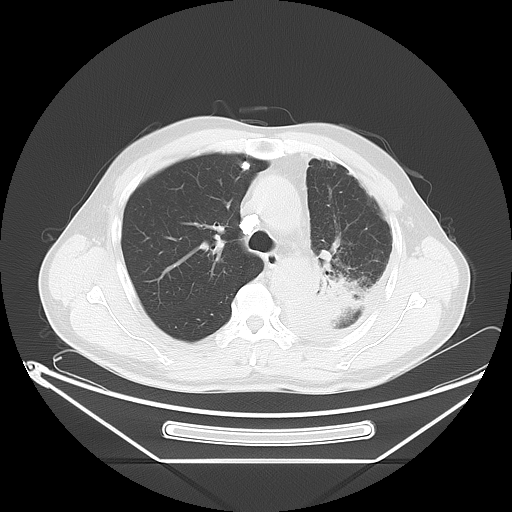
Chest CT, one axial slice. Slice 43 of 63 in the series (ordered by position). Reconstruction kernel LUNG. 120 kVp. Lung window (W 1500 / L -600 HU). 5 mm slice thickness. 512 × 512 image matrix, field of view 442 × 442 mm. Patient: male, 60 years. Case-level facts recorded for this patient, not image findings: clinical TNM (as recorded): T4 N1 M1.
Annotated regions visible in this slice (bounding box drawn by a radiologist):
- lung tumour (recorded histology: adenocarcinoma): bounding box (x1, y1, x2, y2) in pixels: (304, 256, 363, 324)